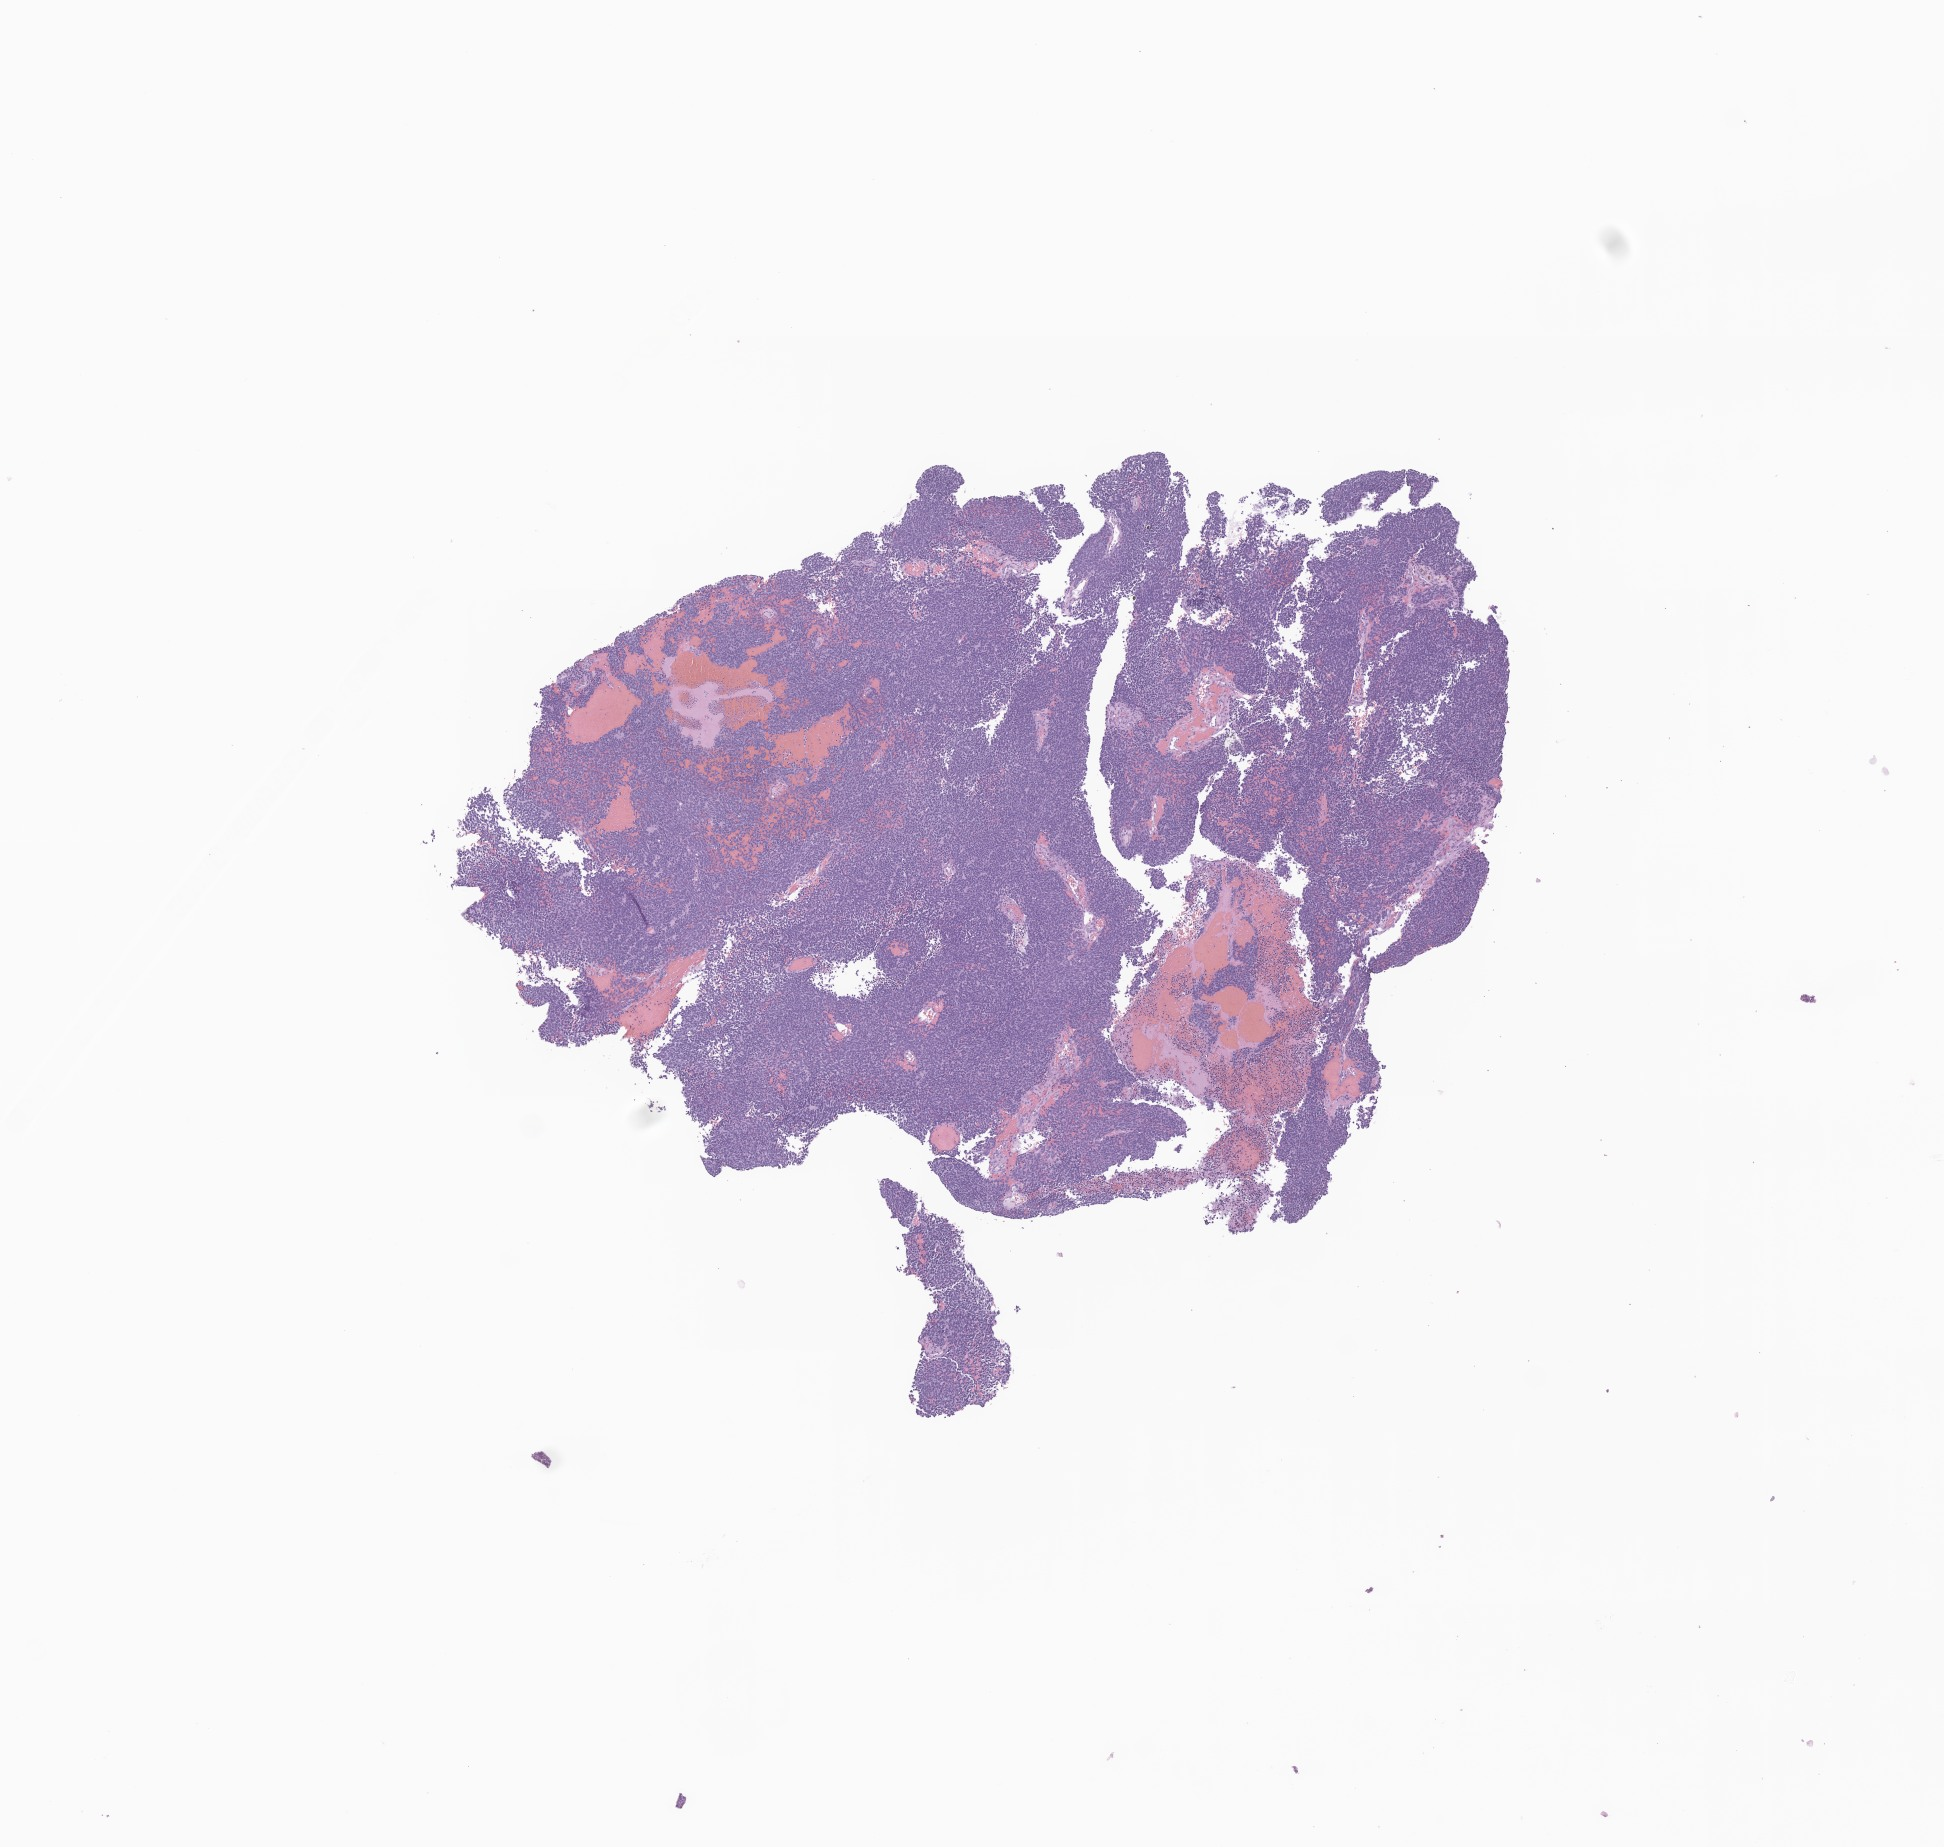
Hematoxylin and eosin (H&E) whole-slide image of tumor tissue from the brain, a low-resolution overview of the entire scanned area, about 8.2 x 7.8 mm. FFPE section. Patient: male, age 177 months (14 years 9 months).
Recorded diagnosis: Medulloblastoma, NOS.